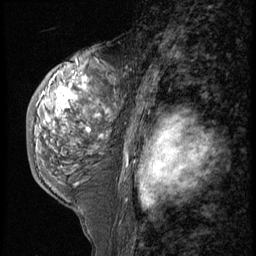
Breast MRI (dynamic contrast-enhanced), one sagittal slice; slice 34 of 56 in the series (ordered by position); 3 images stored at this slice position (order not interpretable as contrast timing); 1.5 T; TE 4.2 ms, TR 9 ms; 256 × 256 image matrix, field of view 180 × 180 mm. Patient: female, 50 years. Case-level facts recorded for this patient, not image findings: setting: breast cancer imaged before/during neoadjuvant chemotherapy; receptor status: triple-negative.
Structures marked on this image (semi-automatically segmented with operator editing):
- analysis volume of interest (the breast-tissue region the enhancement analysis was run in; not a lesion): bounding box <26,50,121,191> (left, top, right, bottom; pixels)
- tumour enhancement mask (voxels above the 140 % enhancement threshold inside the analysis volume of interest): <56,78,97,150>